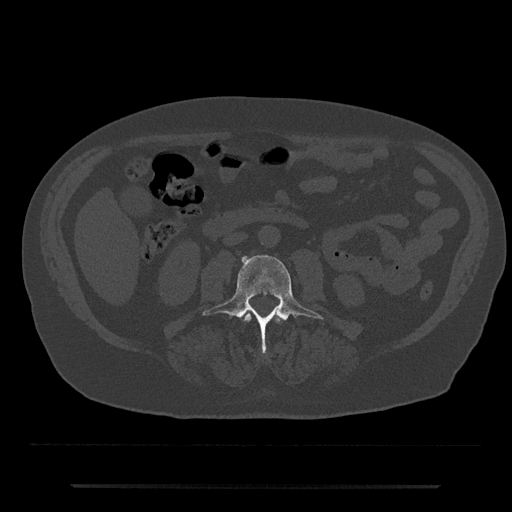
CT including the spine, one axial slice; slice 416 of 797 in the series (ordered by position); reconstruction kernel Br40s/3; 120 kVp; bone window (W 1800 / L 400 HU); 0.5 mm slice thickness; 512 × 512 image matrix, field of view 434 × 434 mm. Patient: male, 80 years. From the clinical record (not read from this slice): primary cancer: prostate; vertebrae with lytic lesions (as recorded): L1, T11.
Structures marked on this image (semi-automatically segmented with operator editing):
- L2 vertebra: box from (x=245, y=315) to (x=282, y=322) px
- L3 vertebra: (x=202, y=255)–(x=323, y=353)